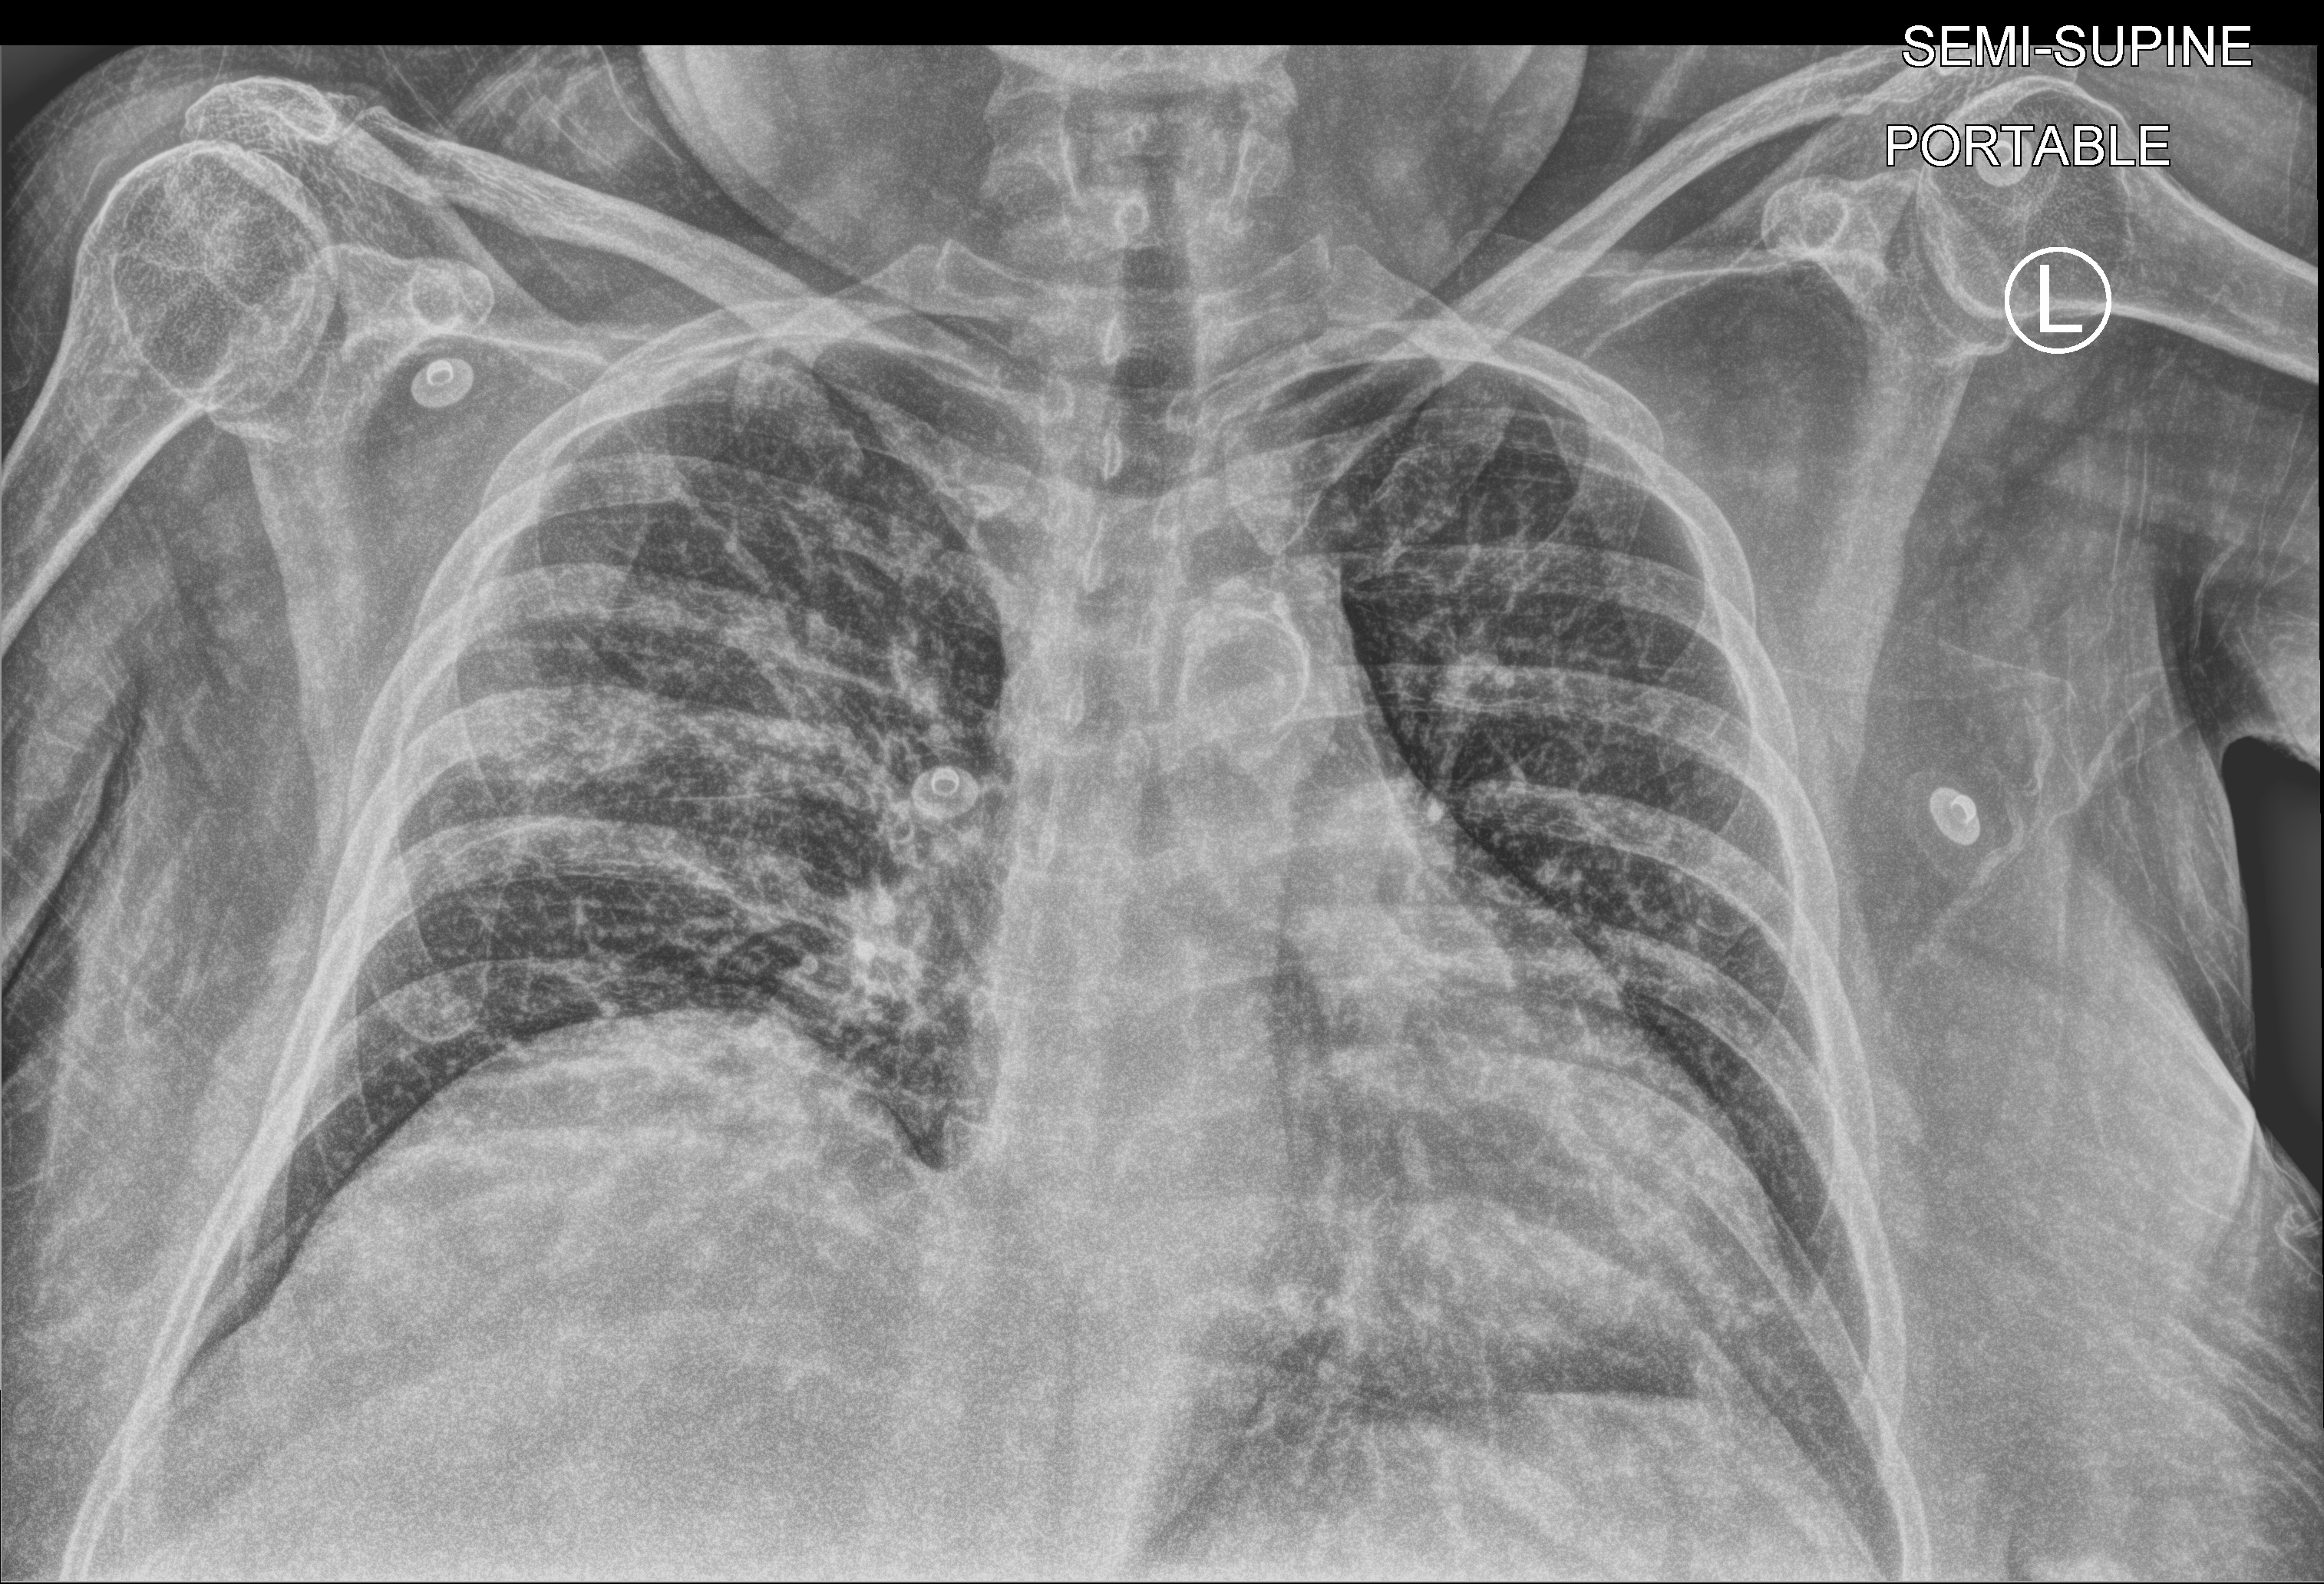
Chest X-ray (portable). Patient hospitalised with COVID-19; female, aged 60–74 years.
From the hospital-stay record, not from the radiograph (when in the stay this image was taken is not recorded):
- admitted to intensive care during this hospital stay: no